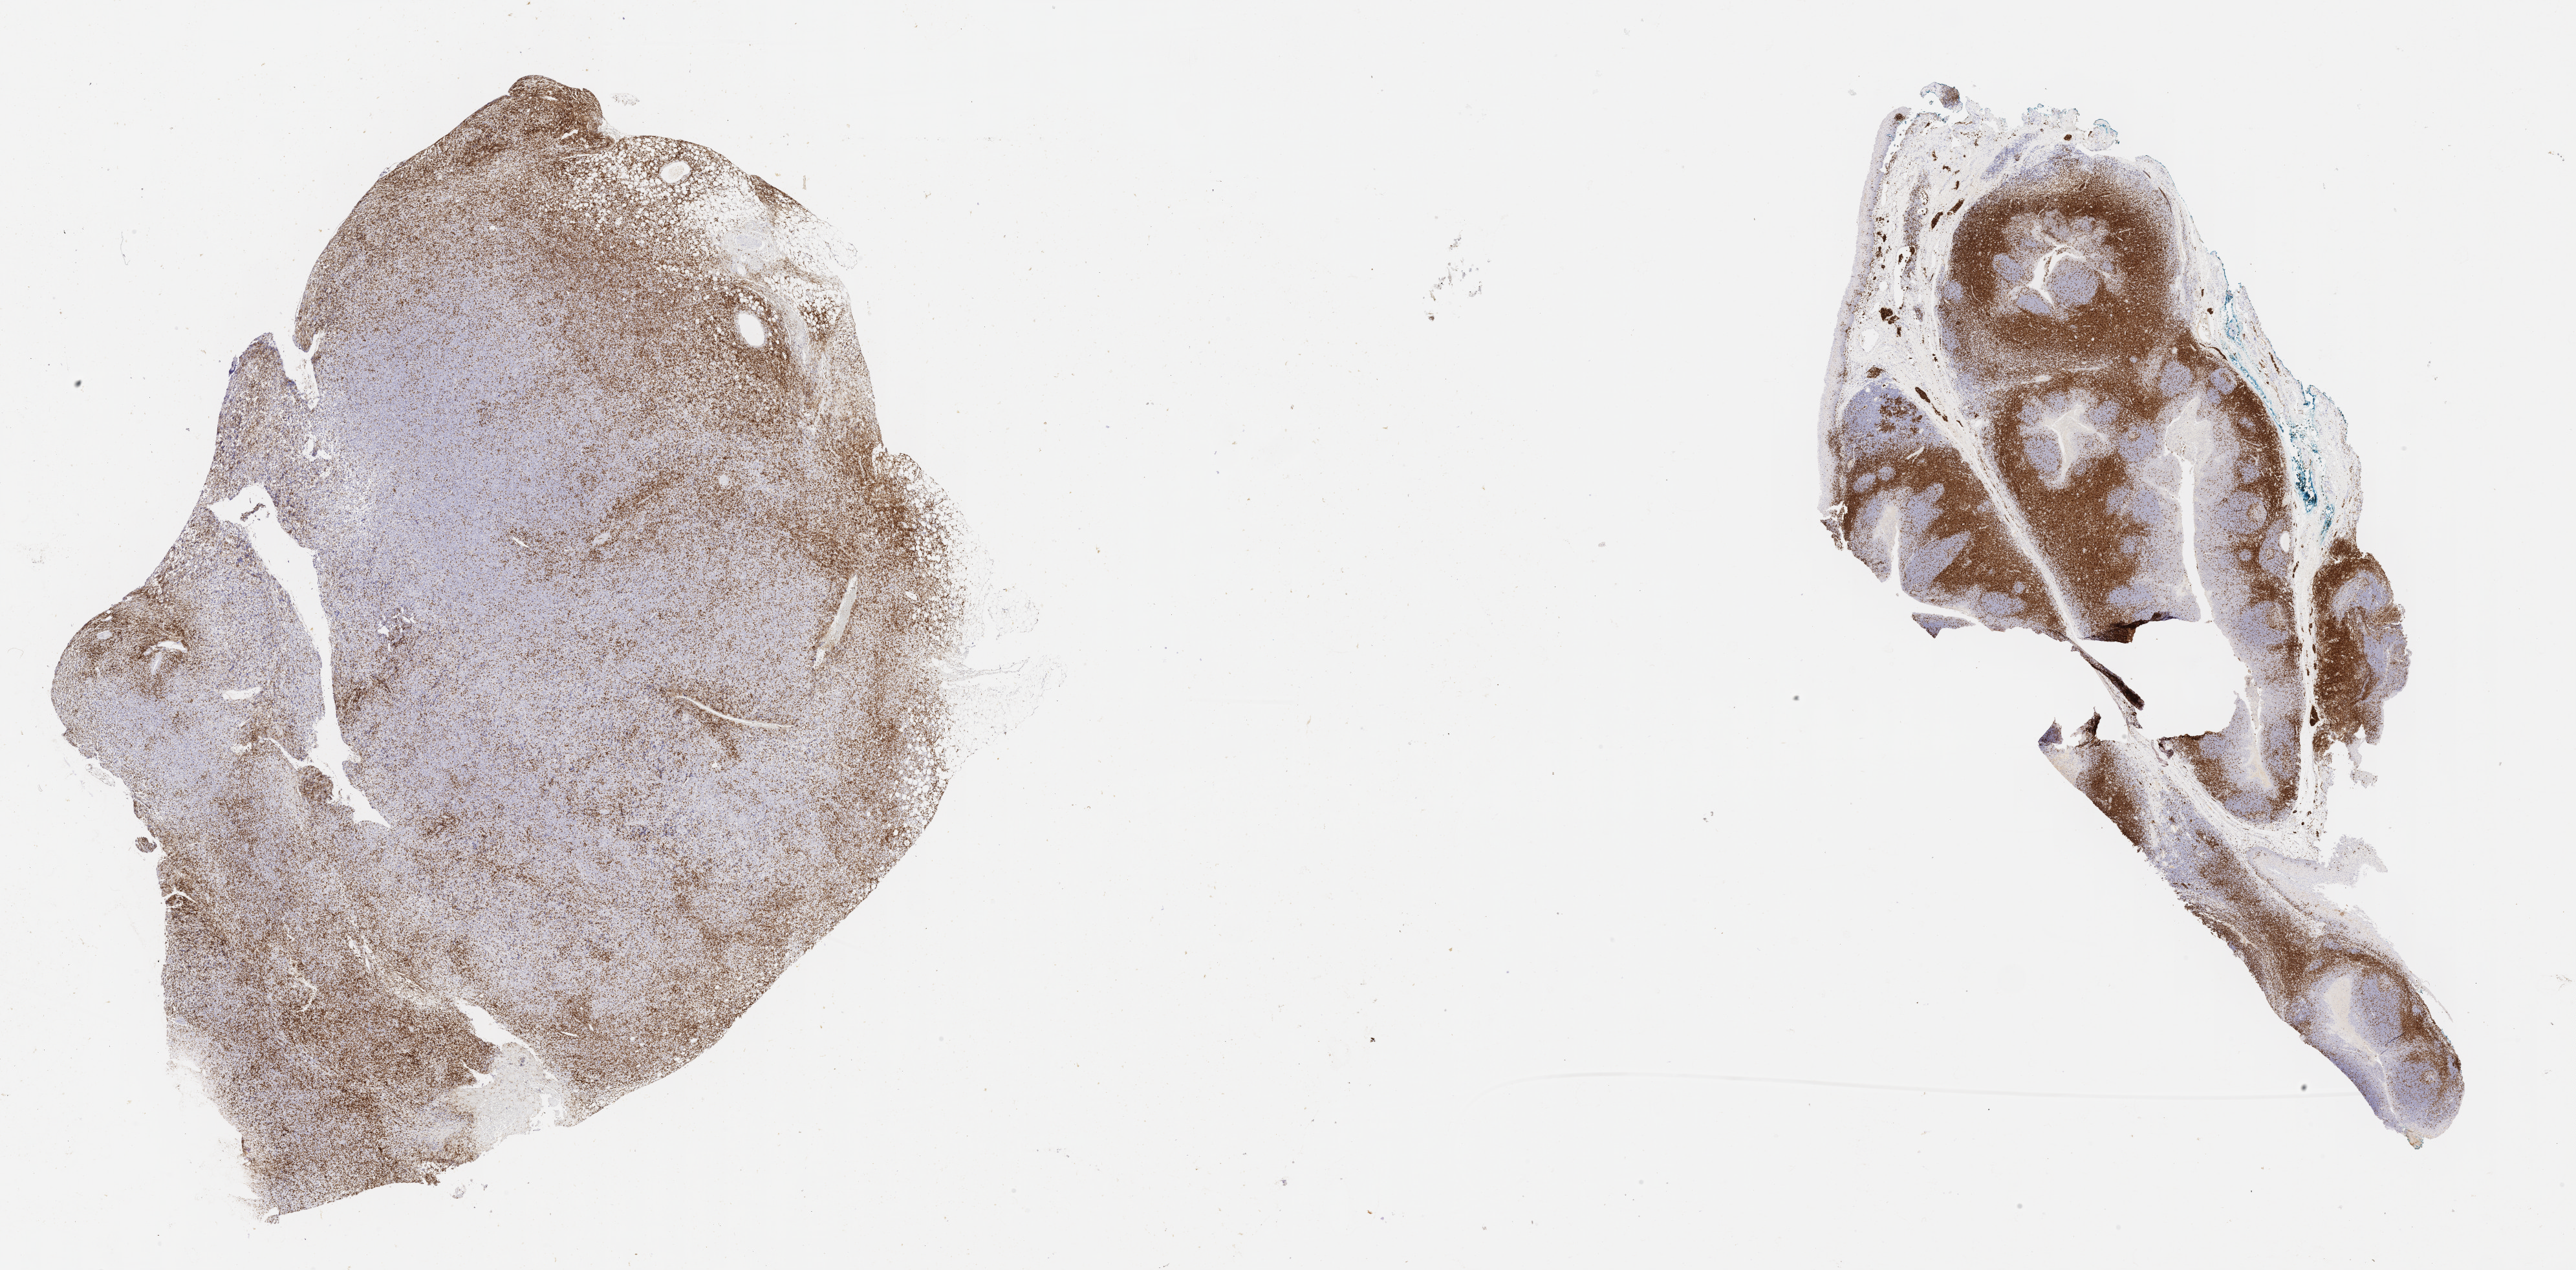
IHC for CD3, whole-slide image, low-resolution overview of the scanned area, about 32.2 x 15.9 mm. Female patient.
Specimen: tumor tissue.